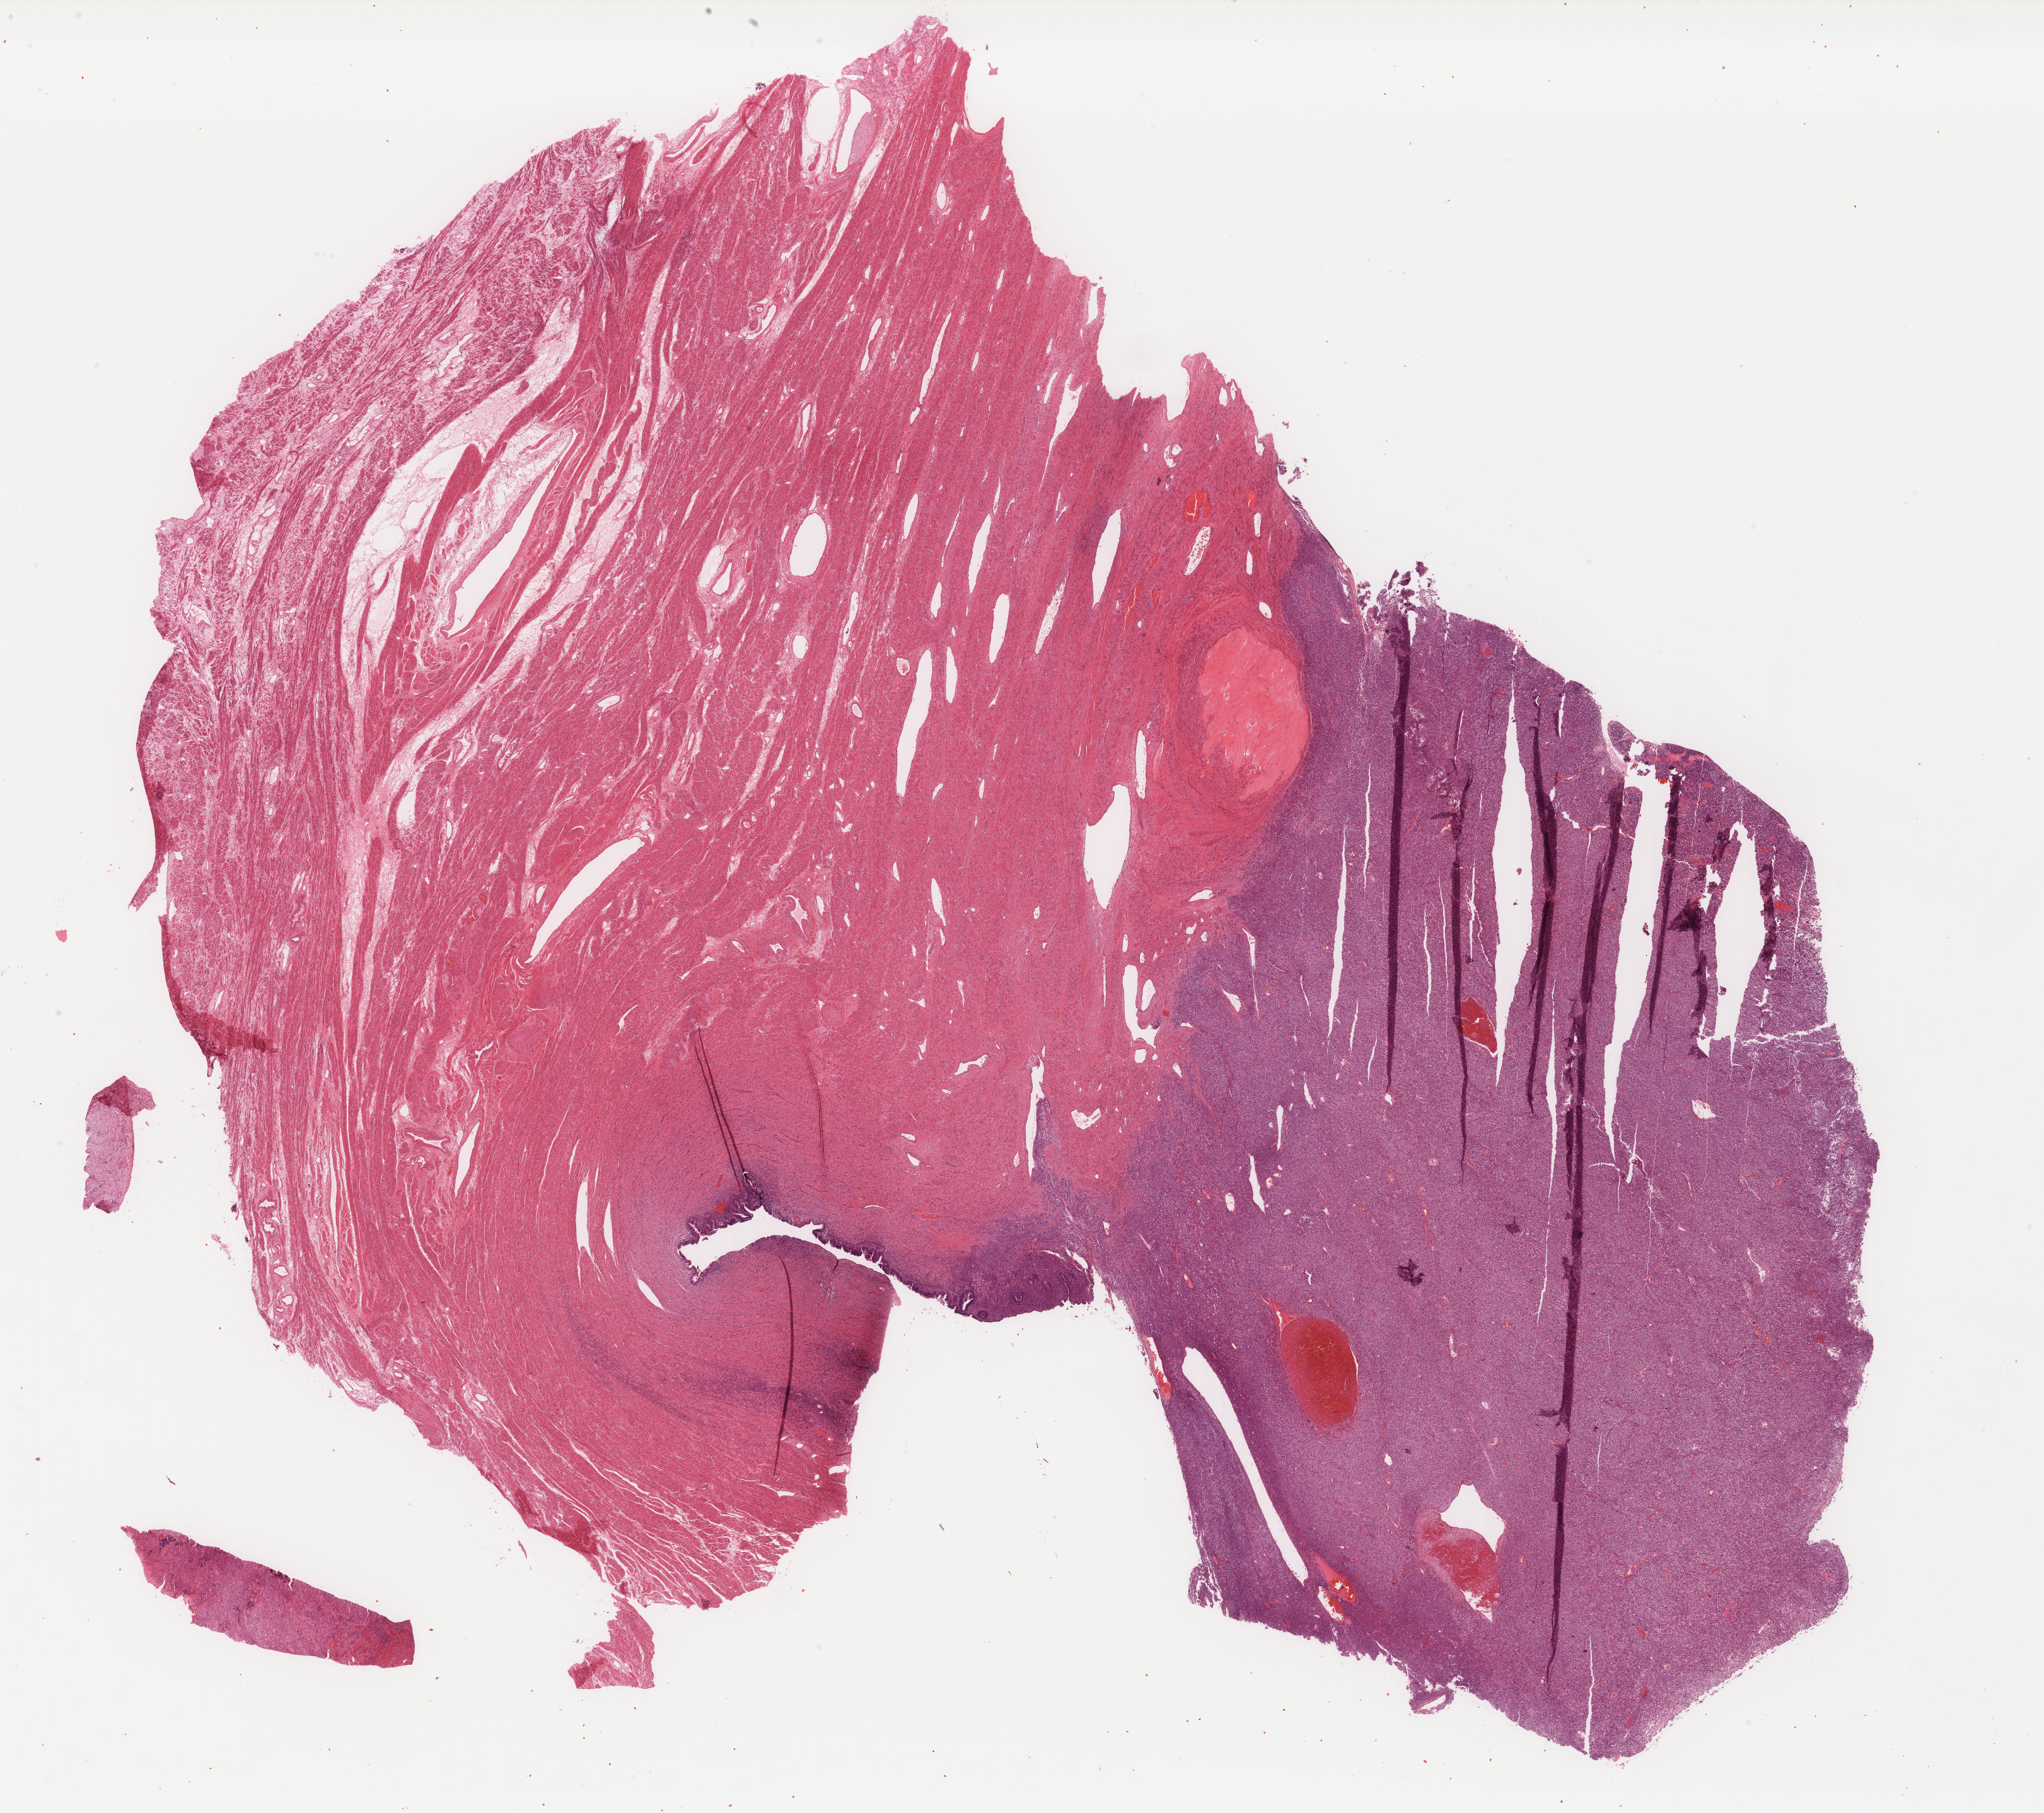
H&E-stained whole-slide image — whole scanned area (about 25.7 x 22.8 mm, slide scanned at 40x) shown as a low-resolution overview, formalin-fixed paraffin-embedded (FFPE) diagnostic section, uterus, primary tumour sample. Female patient; age at initial diagnosis 72 years.
FIGO stage: IVB. Pathologic diagnosis: Mullerian mixed tumor.